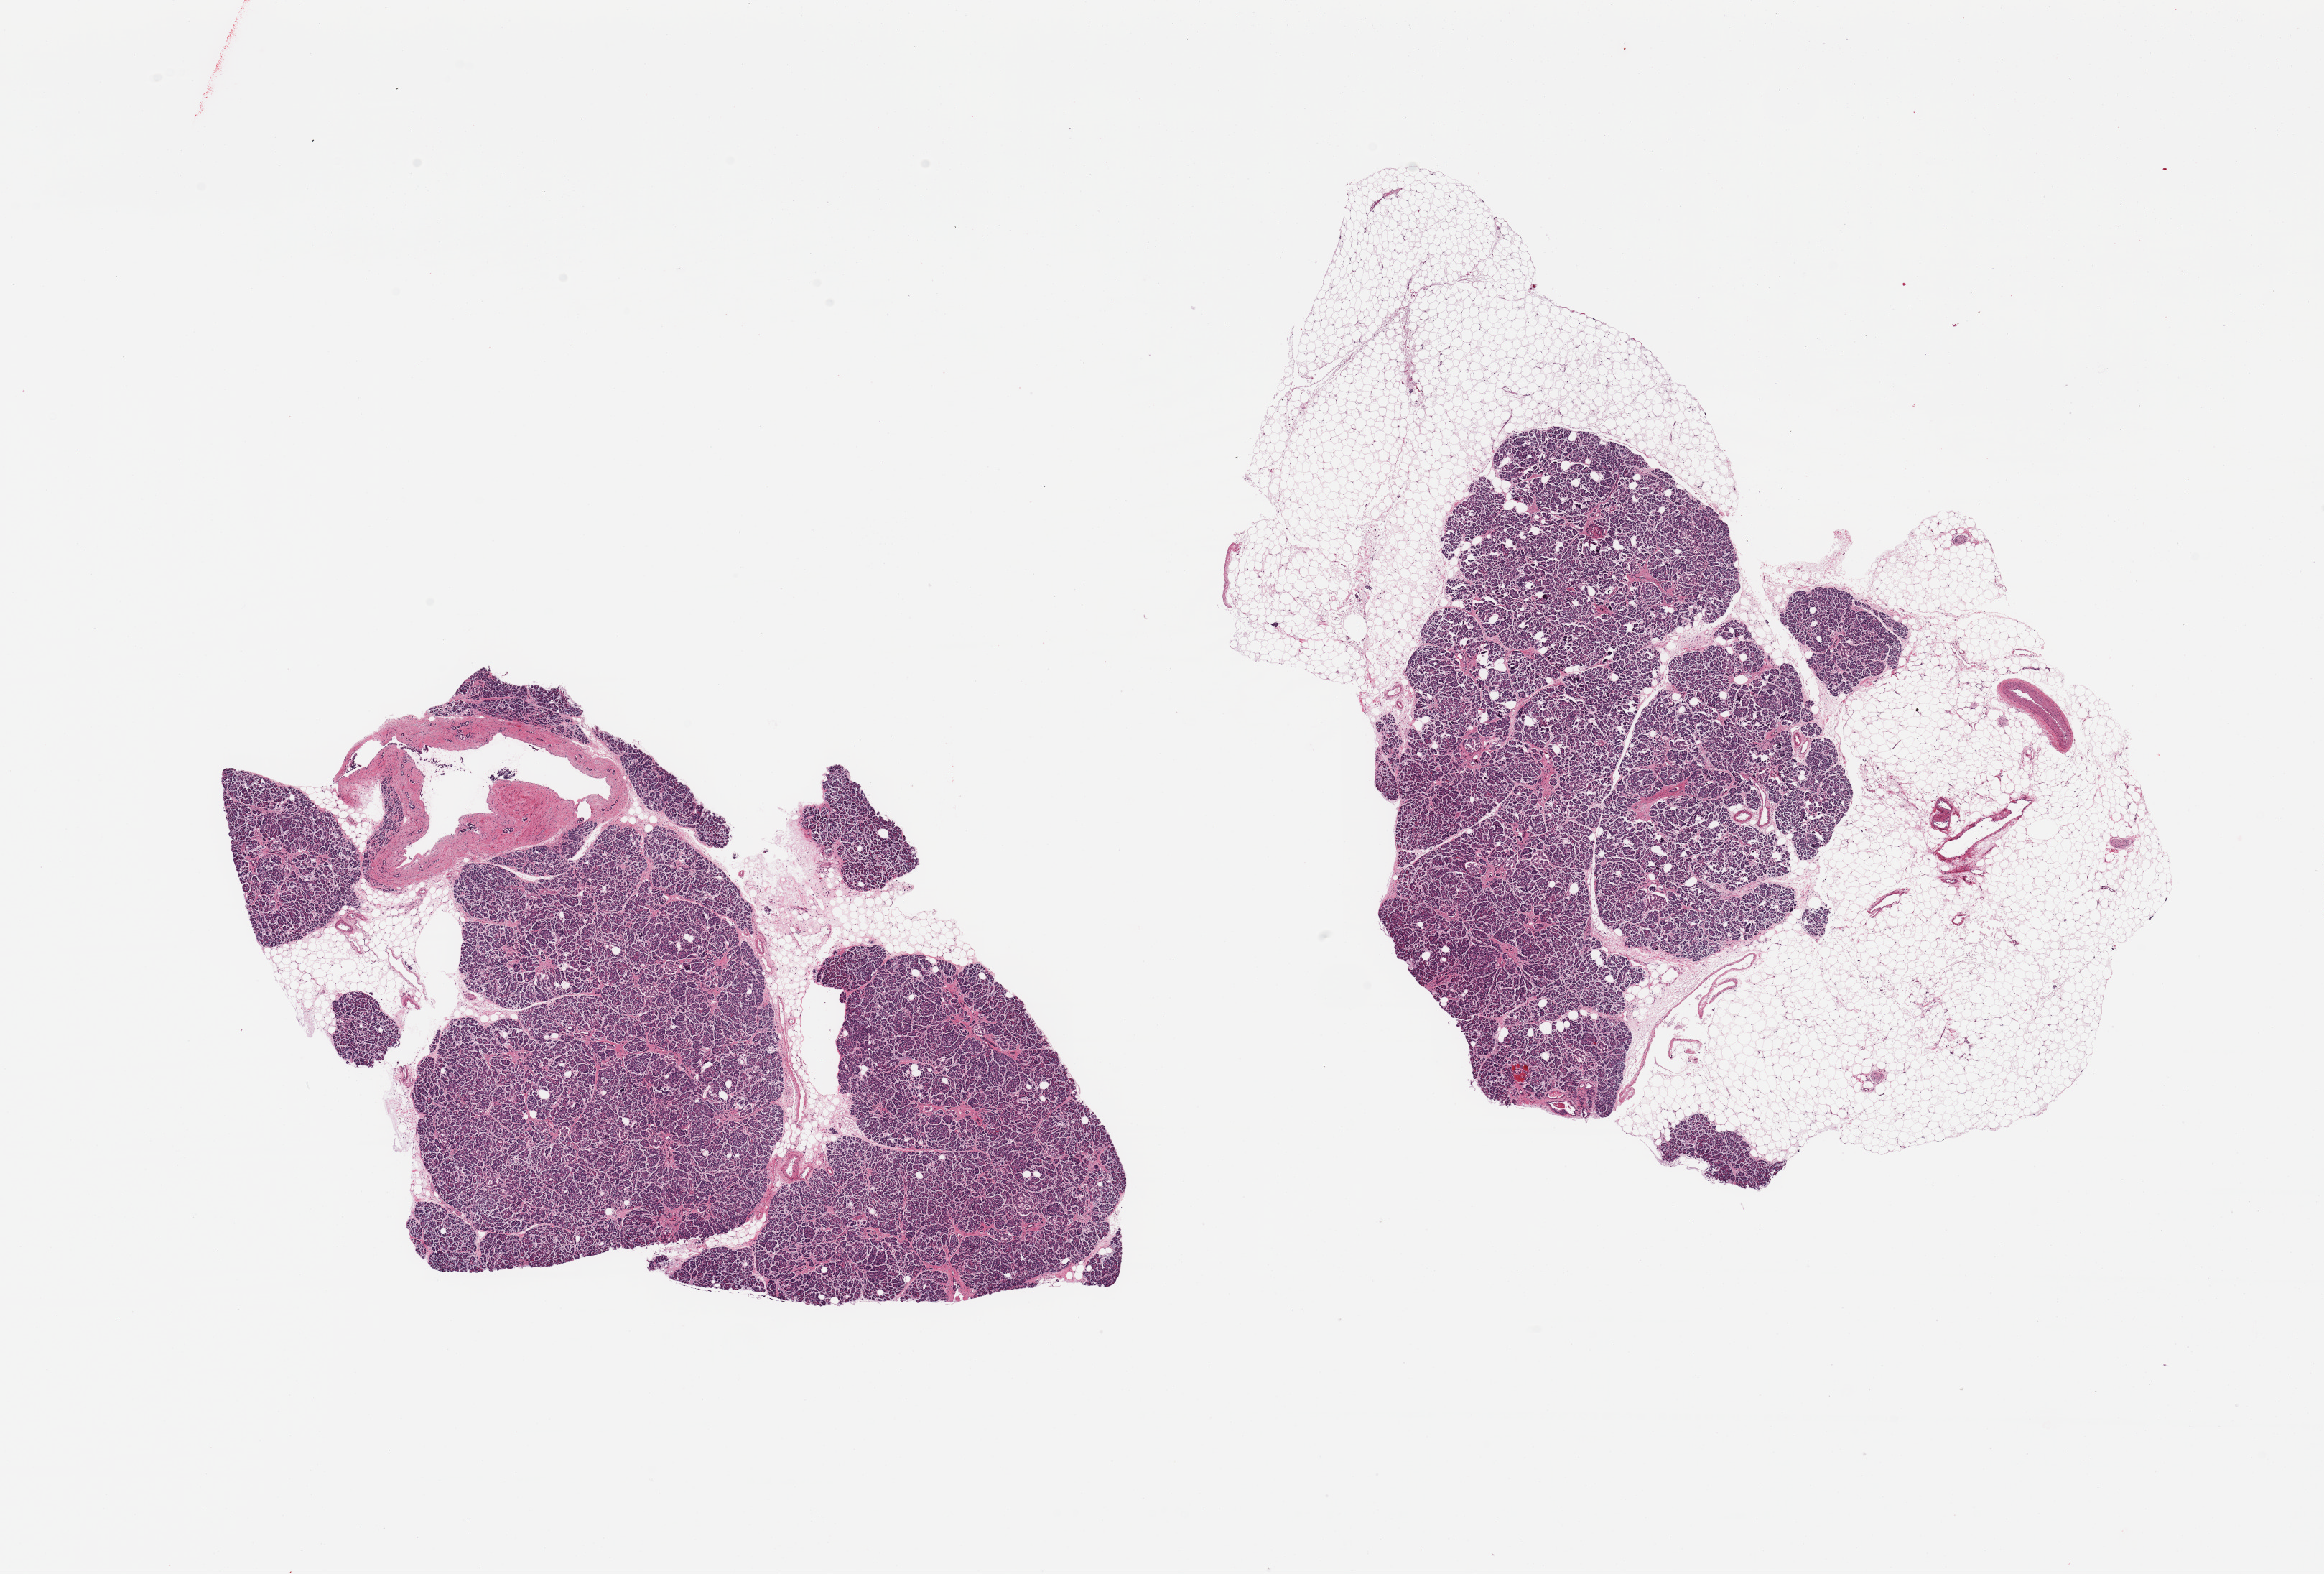
Whole-slide image, H&E stain, low-resolution overview of the scanned area, about 25.6 x 17.3 mm, PAXgene-fixed, paraffin-embedded tissue, section of pancreas (target tissue), tissue donor sample.
Review note (as recorded): 2 pieces; 40% external fat on 1; 10% fat & large duct on other.